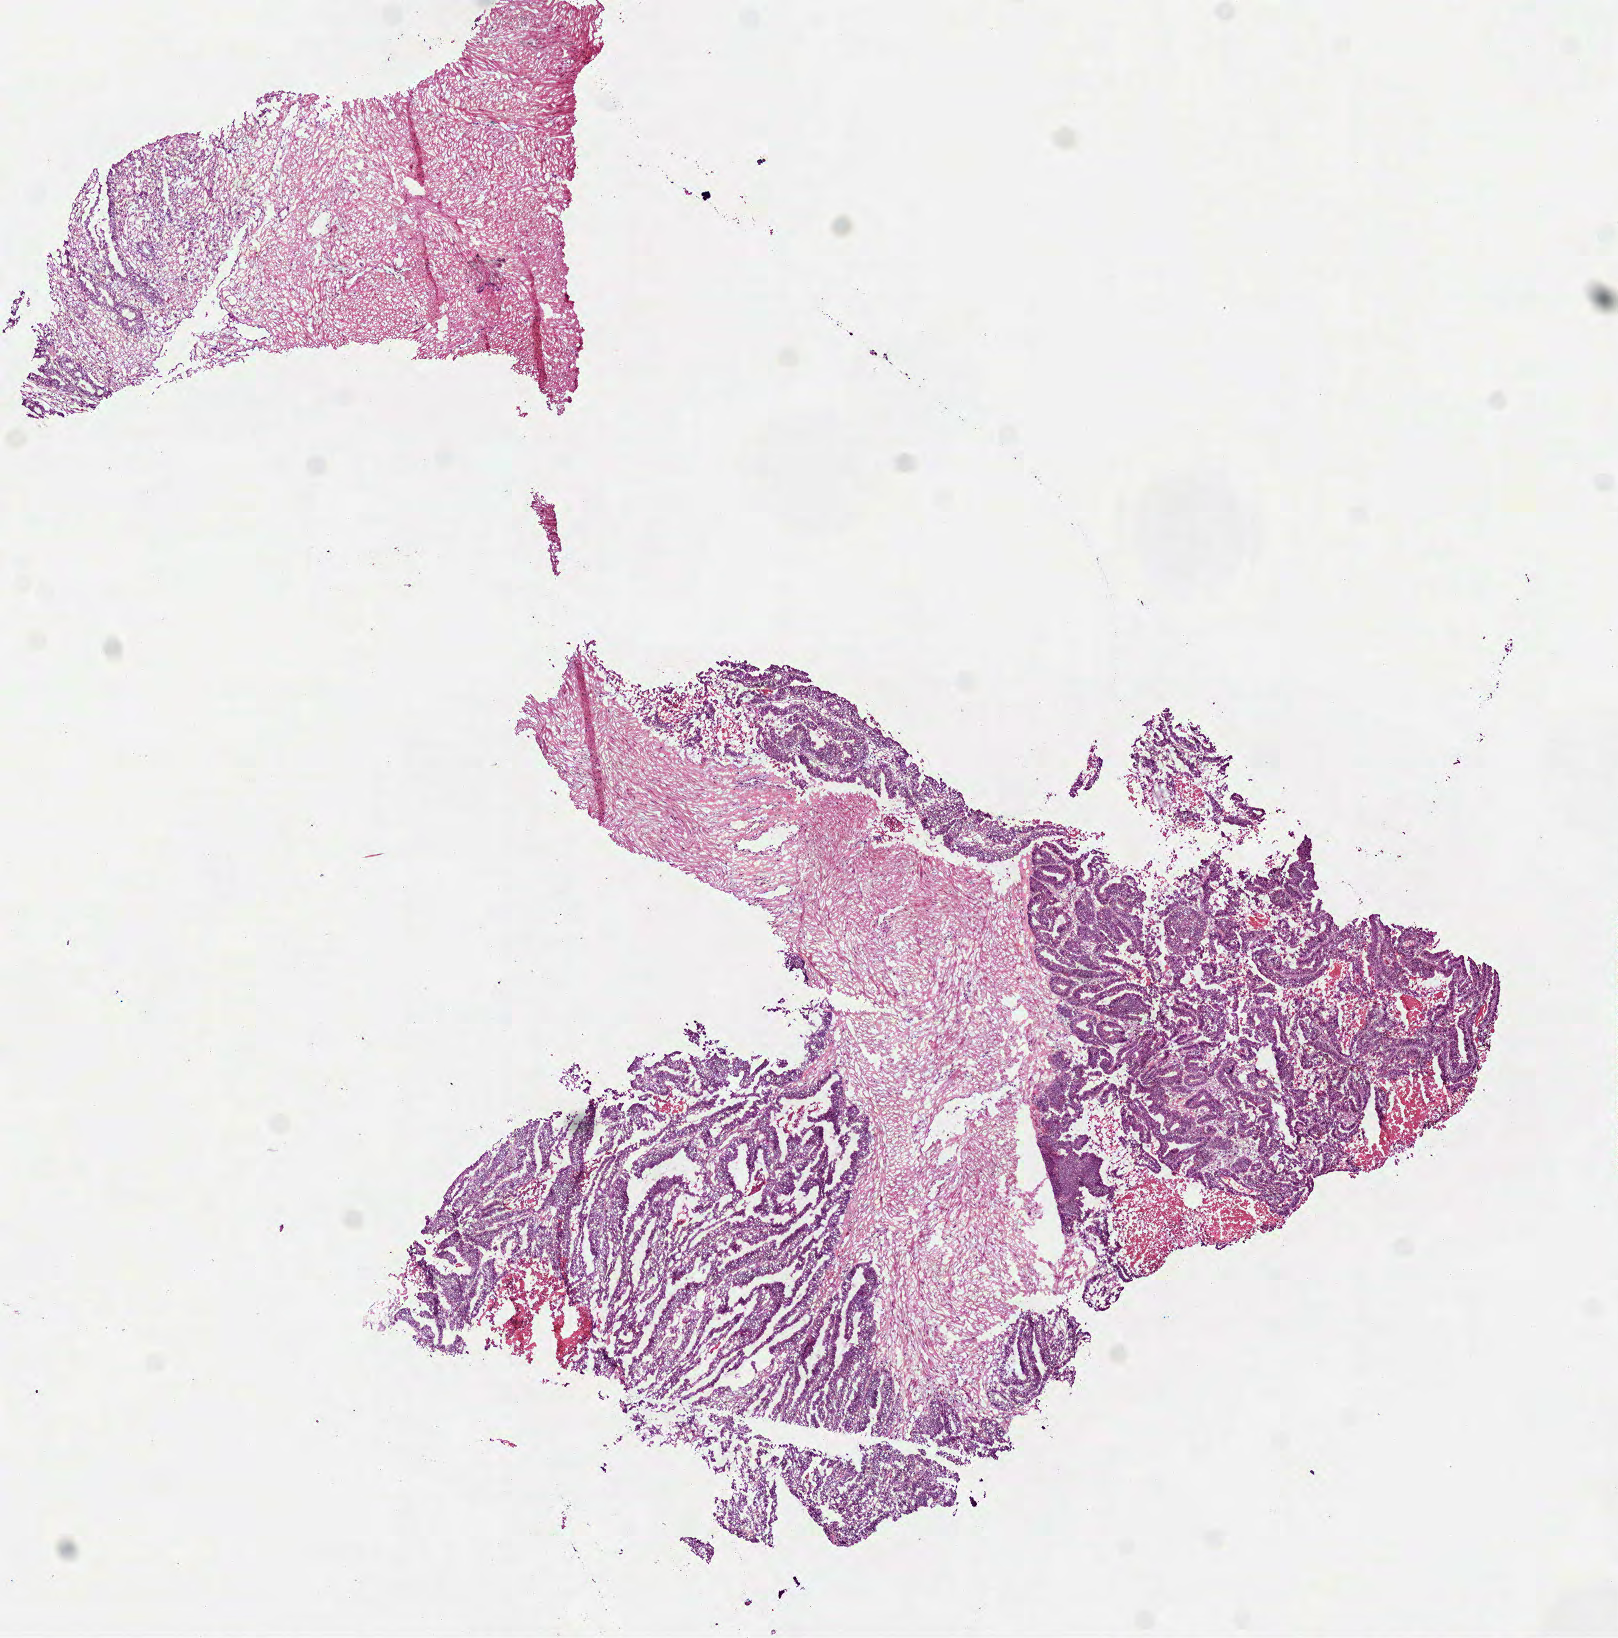
Hematoxylin and eosin (H&E) stained whole-slide image — shown as a low-resolution overview of the whole scanned area (about 6.5 x 6.6 mm). Frozen section. Sample: primary tumour, colon. Patient: male, age at initial diagnosis 59 years. Pathologist review of this section (percent, as recorded): tumour cells 65%, tumour nuclei 80%, normal cells 25%, stromal cells 0%, necrosis 10%. Inflammatory infiltration, as recorded: lymphocyte infiltration 2%, monocyte infiltration 1%, neutrophil infiltration 1%.
• AJCC pathologic stage: IVA
• TNM: T3 N0 M1
• histologic diagnosis: Adenocarcinoma, NOS